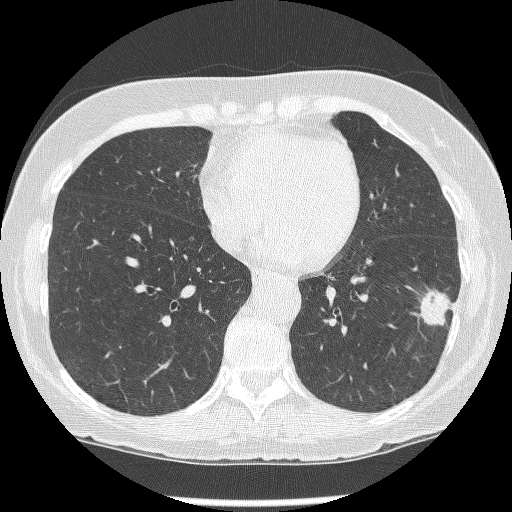
Axial slice from a low-dose chest CT screening exam, first (baseline) screen, lung window (W 1500 / L -600 HU), 1.25 mm slice thickness, slice 92 of 247 in the series, 512 × 512 image matrix. Female, age 62 years at enrolment.
Expert reader's lesion annotation, bounding box <418,283,461,334> (left, top, right, bottom; pixels). The screening reader recorded 2 non-calcified nodules or masses ≥4 mm on this exam (left lower lobe, left lower lobe); which of them this box marks is not recorded. Participant outcome: lung cancer diagnosed 15 days after this screen — non-small cell carcinoma, left lower lobe, stage IIIB (AJCC 6th edition), 23 mm at pathology.